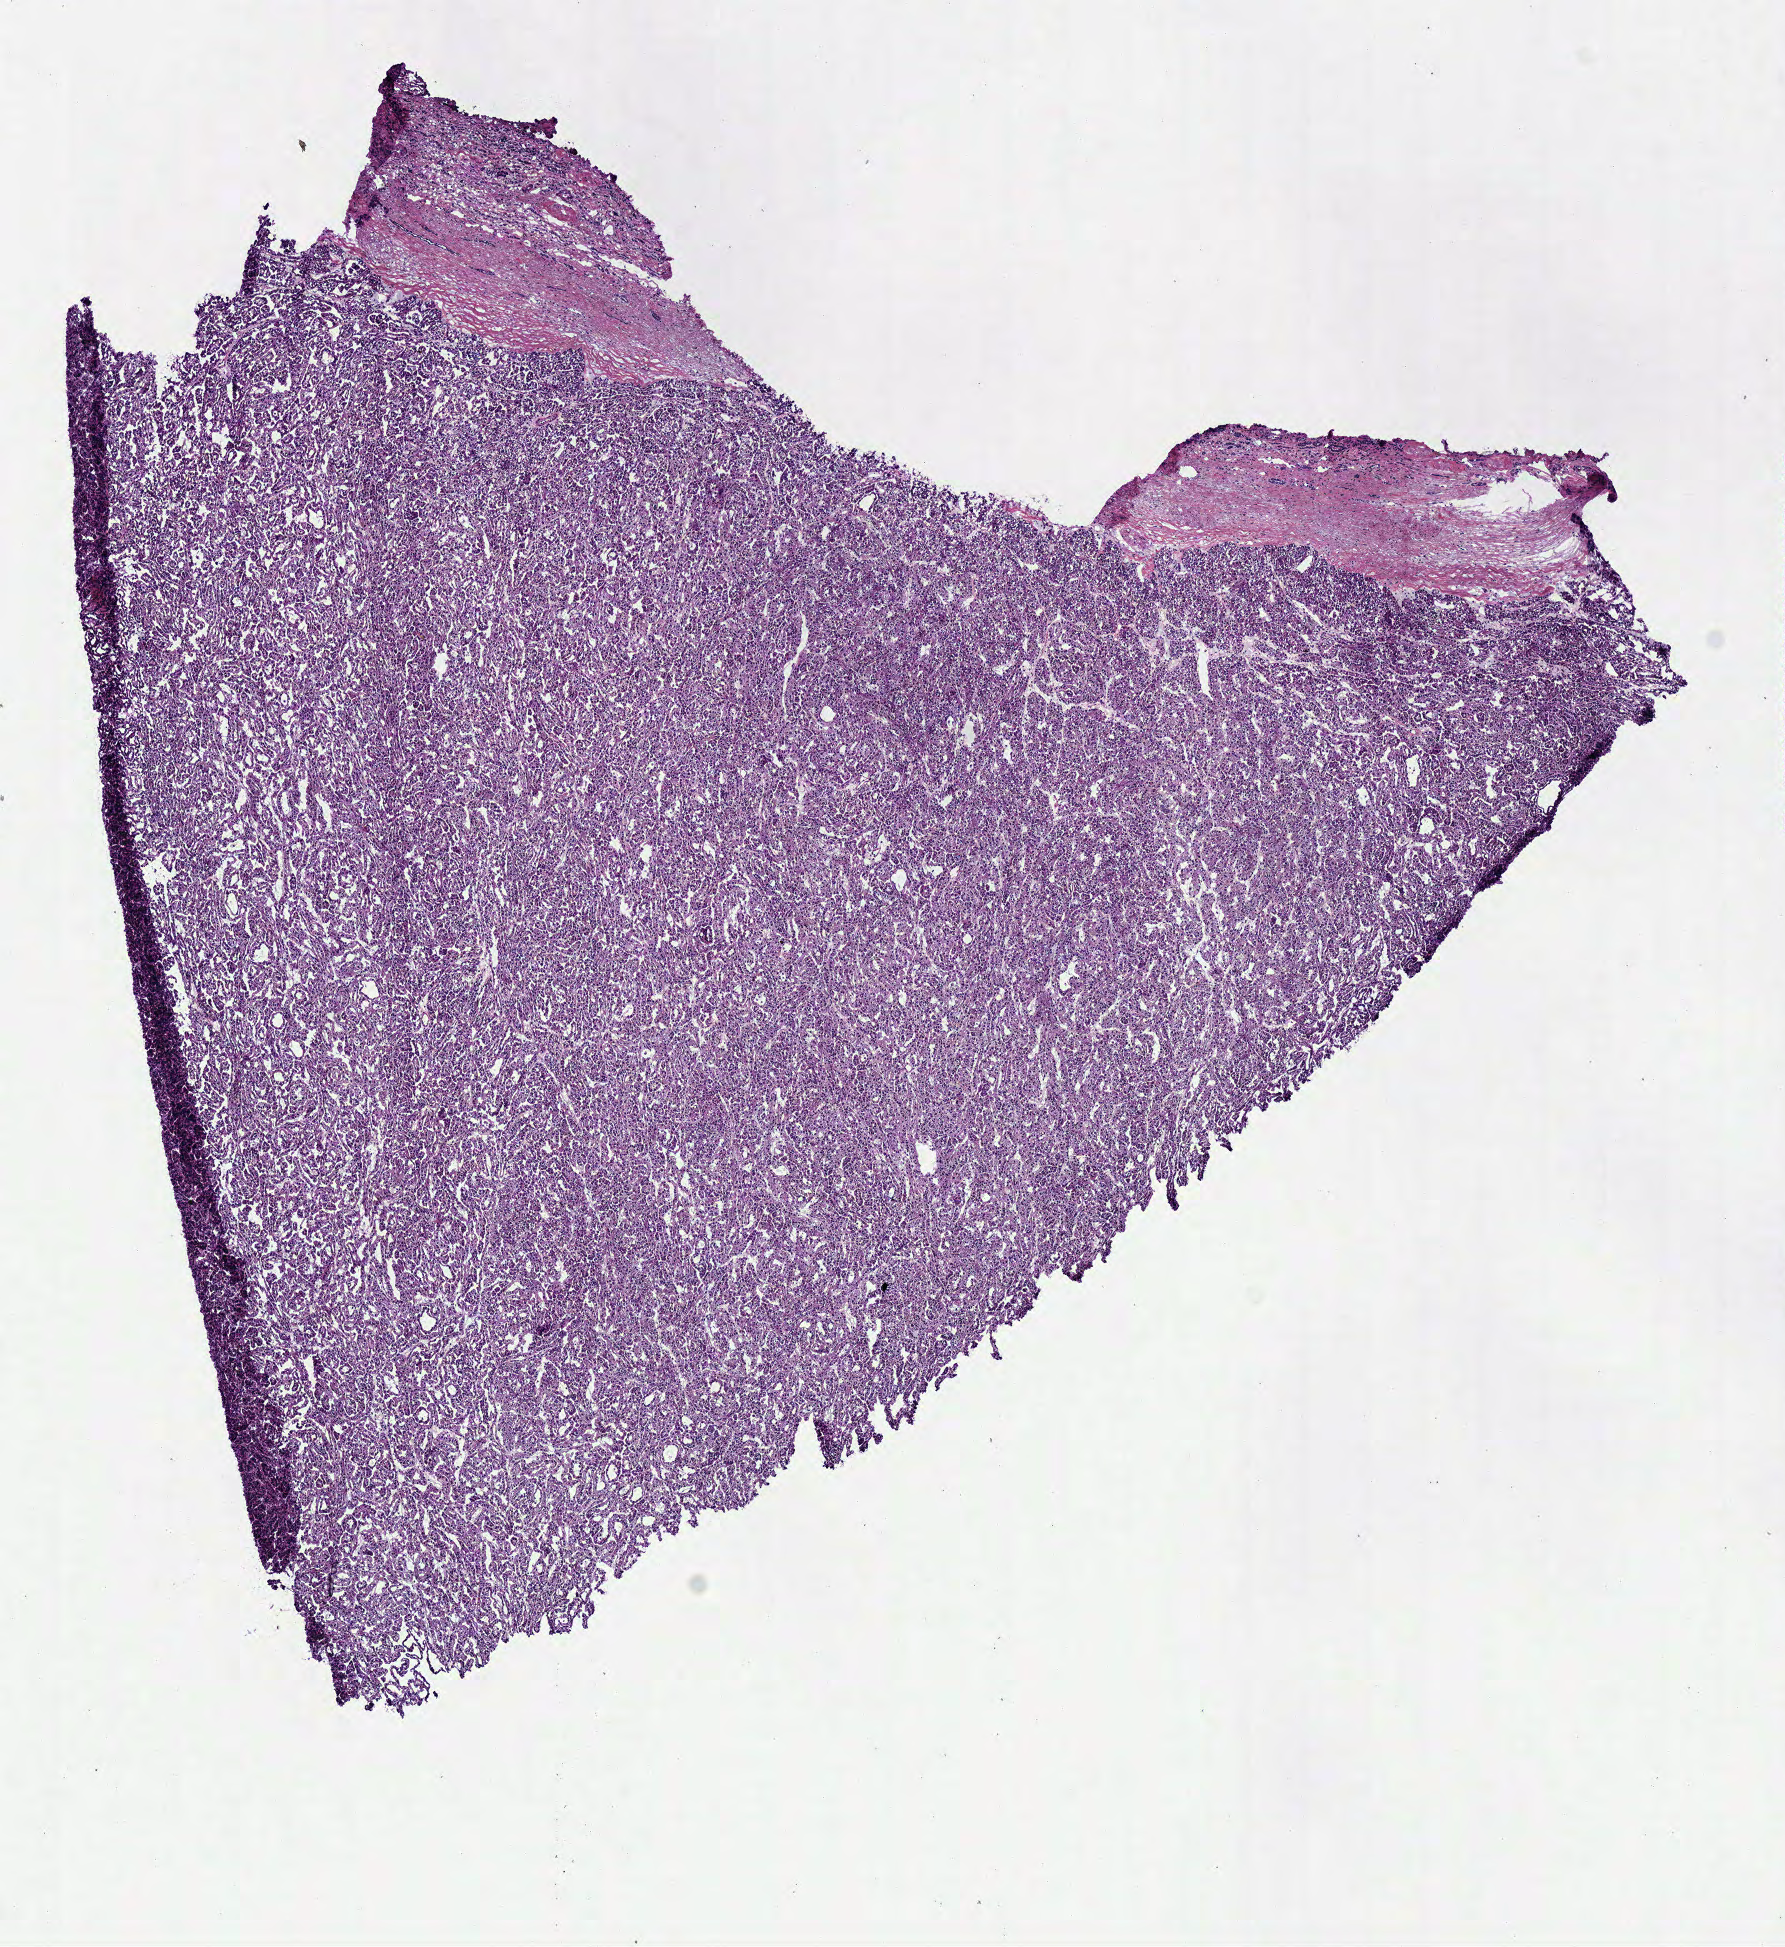
Hematoxylin and eosin (H&E) stained whole-slide image — a low-resolution overview of the entire scanned area, about 7.0 x 7.7 mm. Frozen section from the bottom of the tissue portion. Sample: primary tumour, kidney. Patient: female, age at initial diagnosis 66 years. Pathologist review of this section (percent, as recorded): tumour cells 90%, tumour nuclei 85%, normal cells 0%, stromal cells 10%, necrosis 0%.
Laterality: right. Pathologic diagnosis: Papillary adenocarcinoma, NOS. AJCC pathologic stage: I (6th edition).